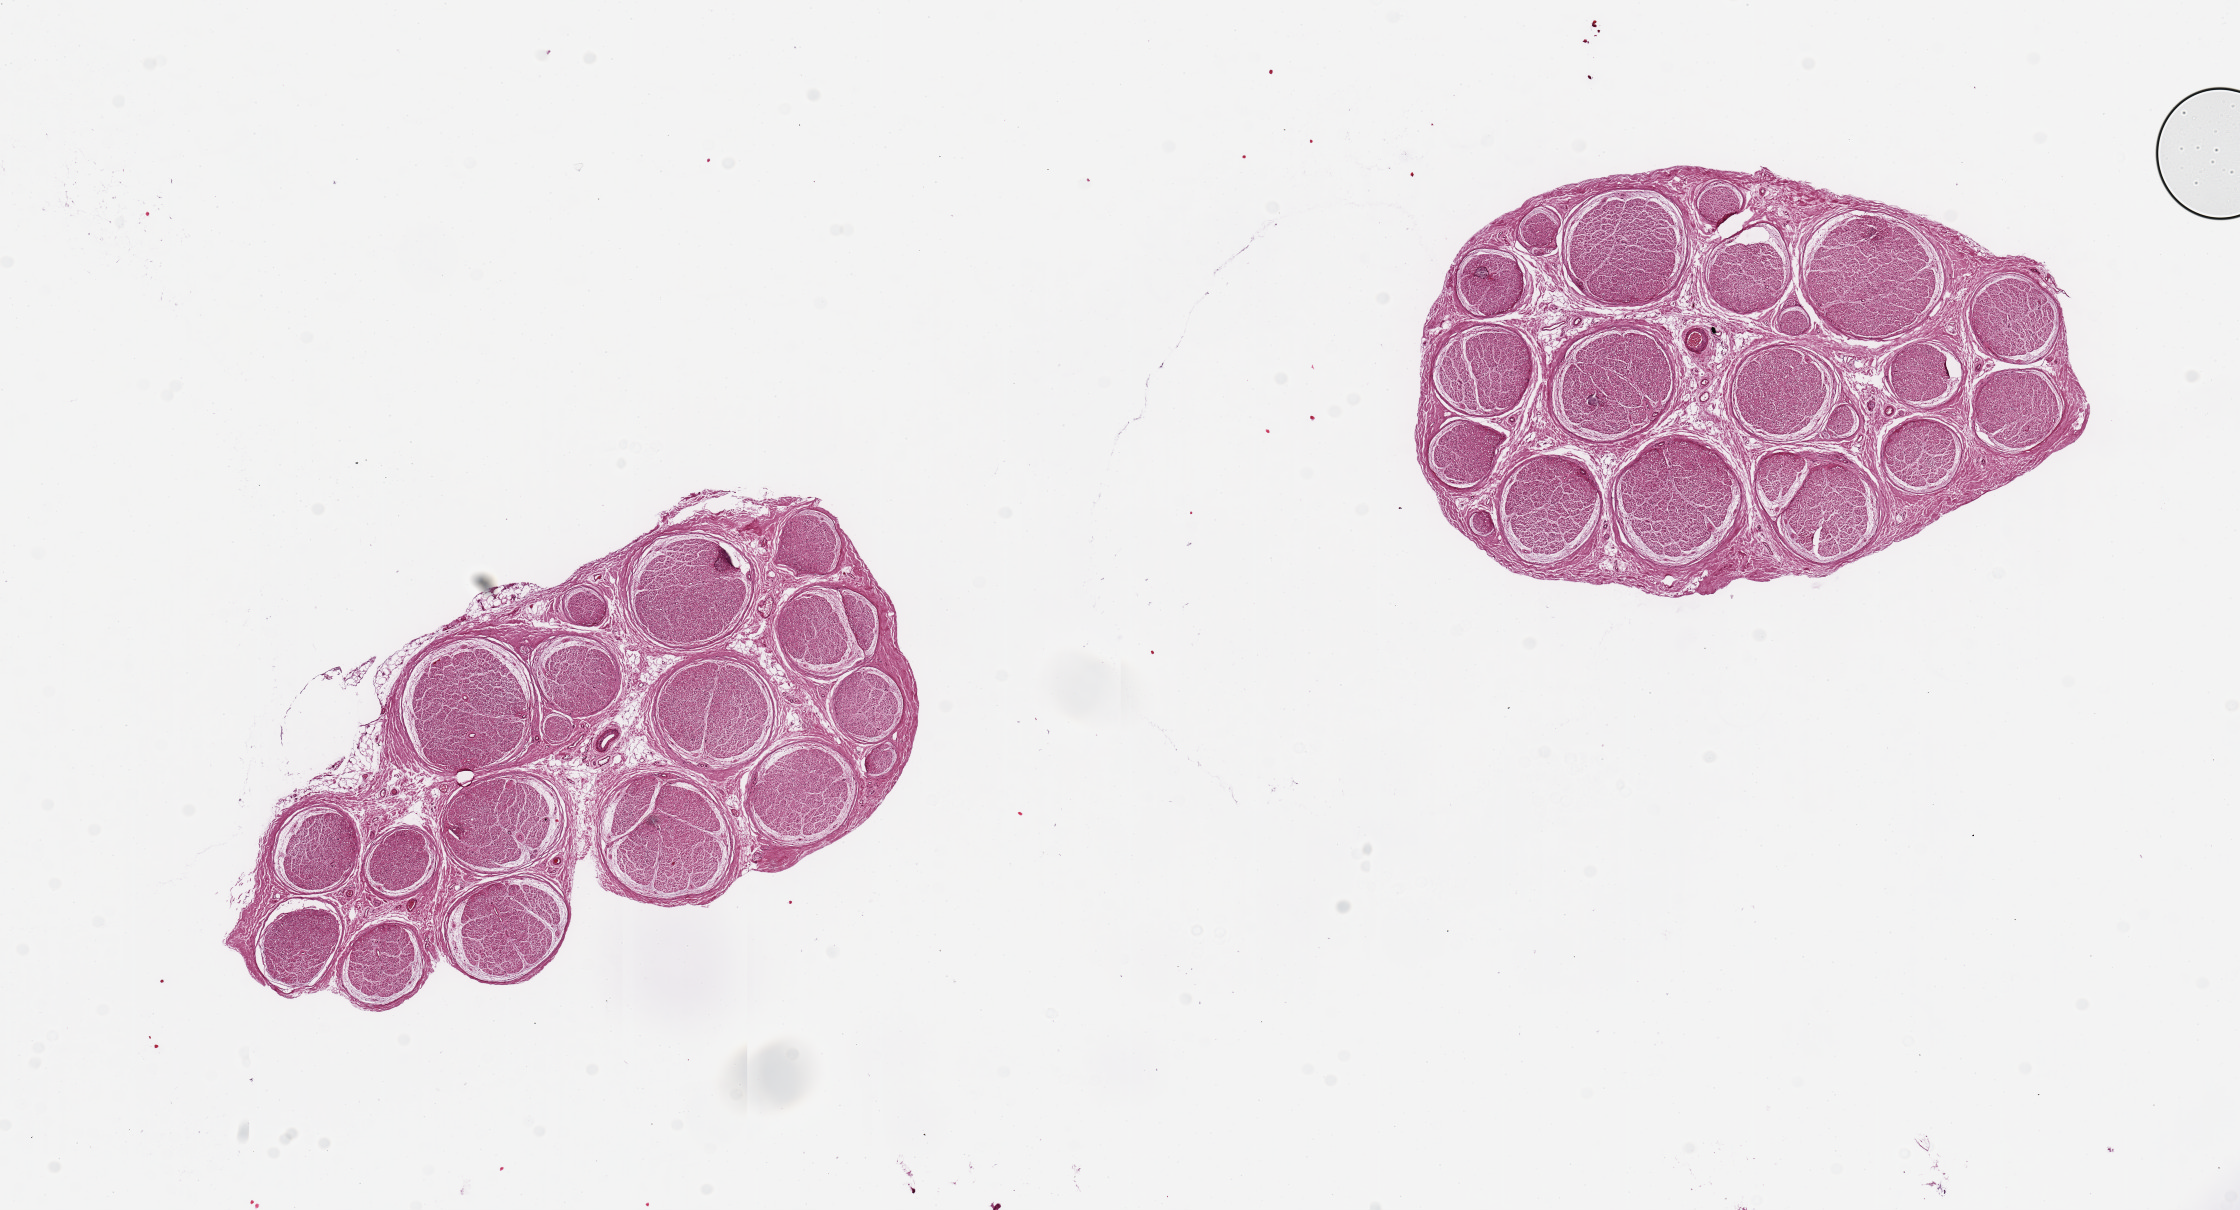
Whole-slide image, H&E stain — whole scanned area (about 17.7 x 9.6 mm) shown as a low-resolution overview; PAXgene-fixed, paraffin-embedded tissue; sampled site (target tissue): tibial nerve; tissue donor sample.
Pathologist's review note for this sample: 2 pieces 6x3 & 5x3 mm; virtually fat free.